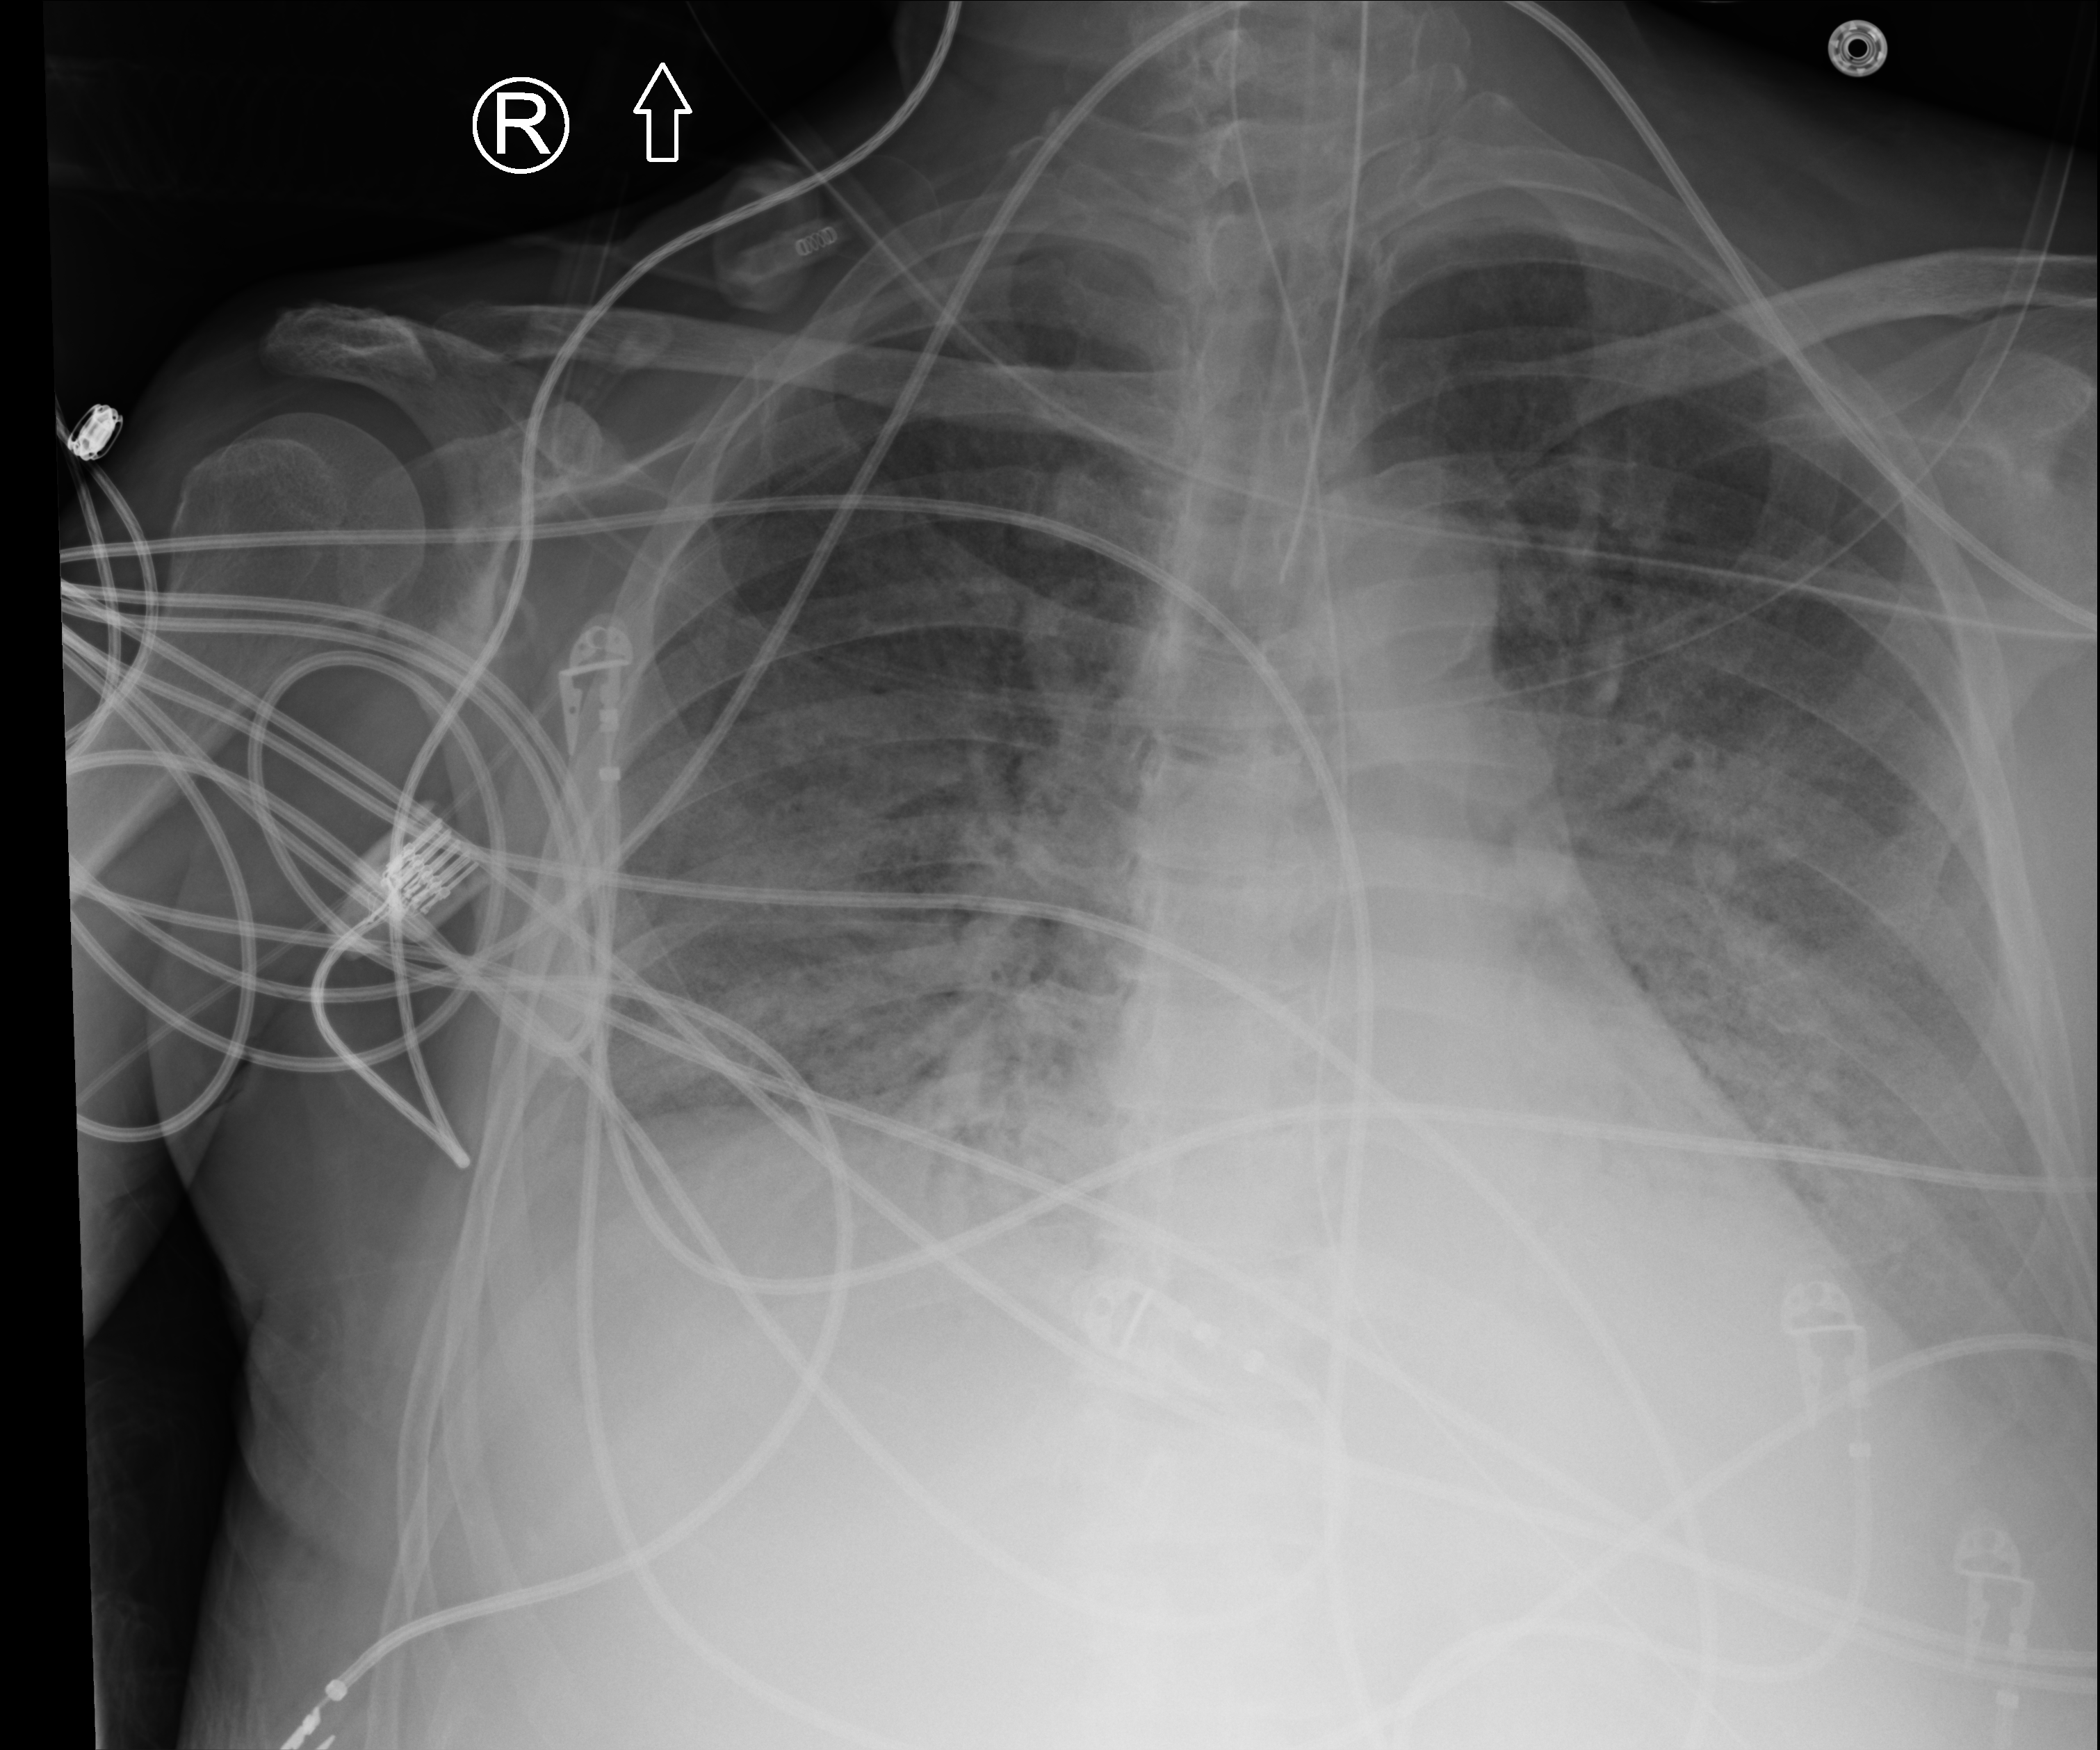
Bedside chest radiograph (computed radiography), anteroposterior (AP) projection. Male patient hospitalised with COVID-19, age 60–74 years.
Hospital-stay facts (about this admission, not read from this image; timing relative to this image not recorded): other chronic lung disease (admission record): no.